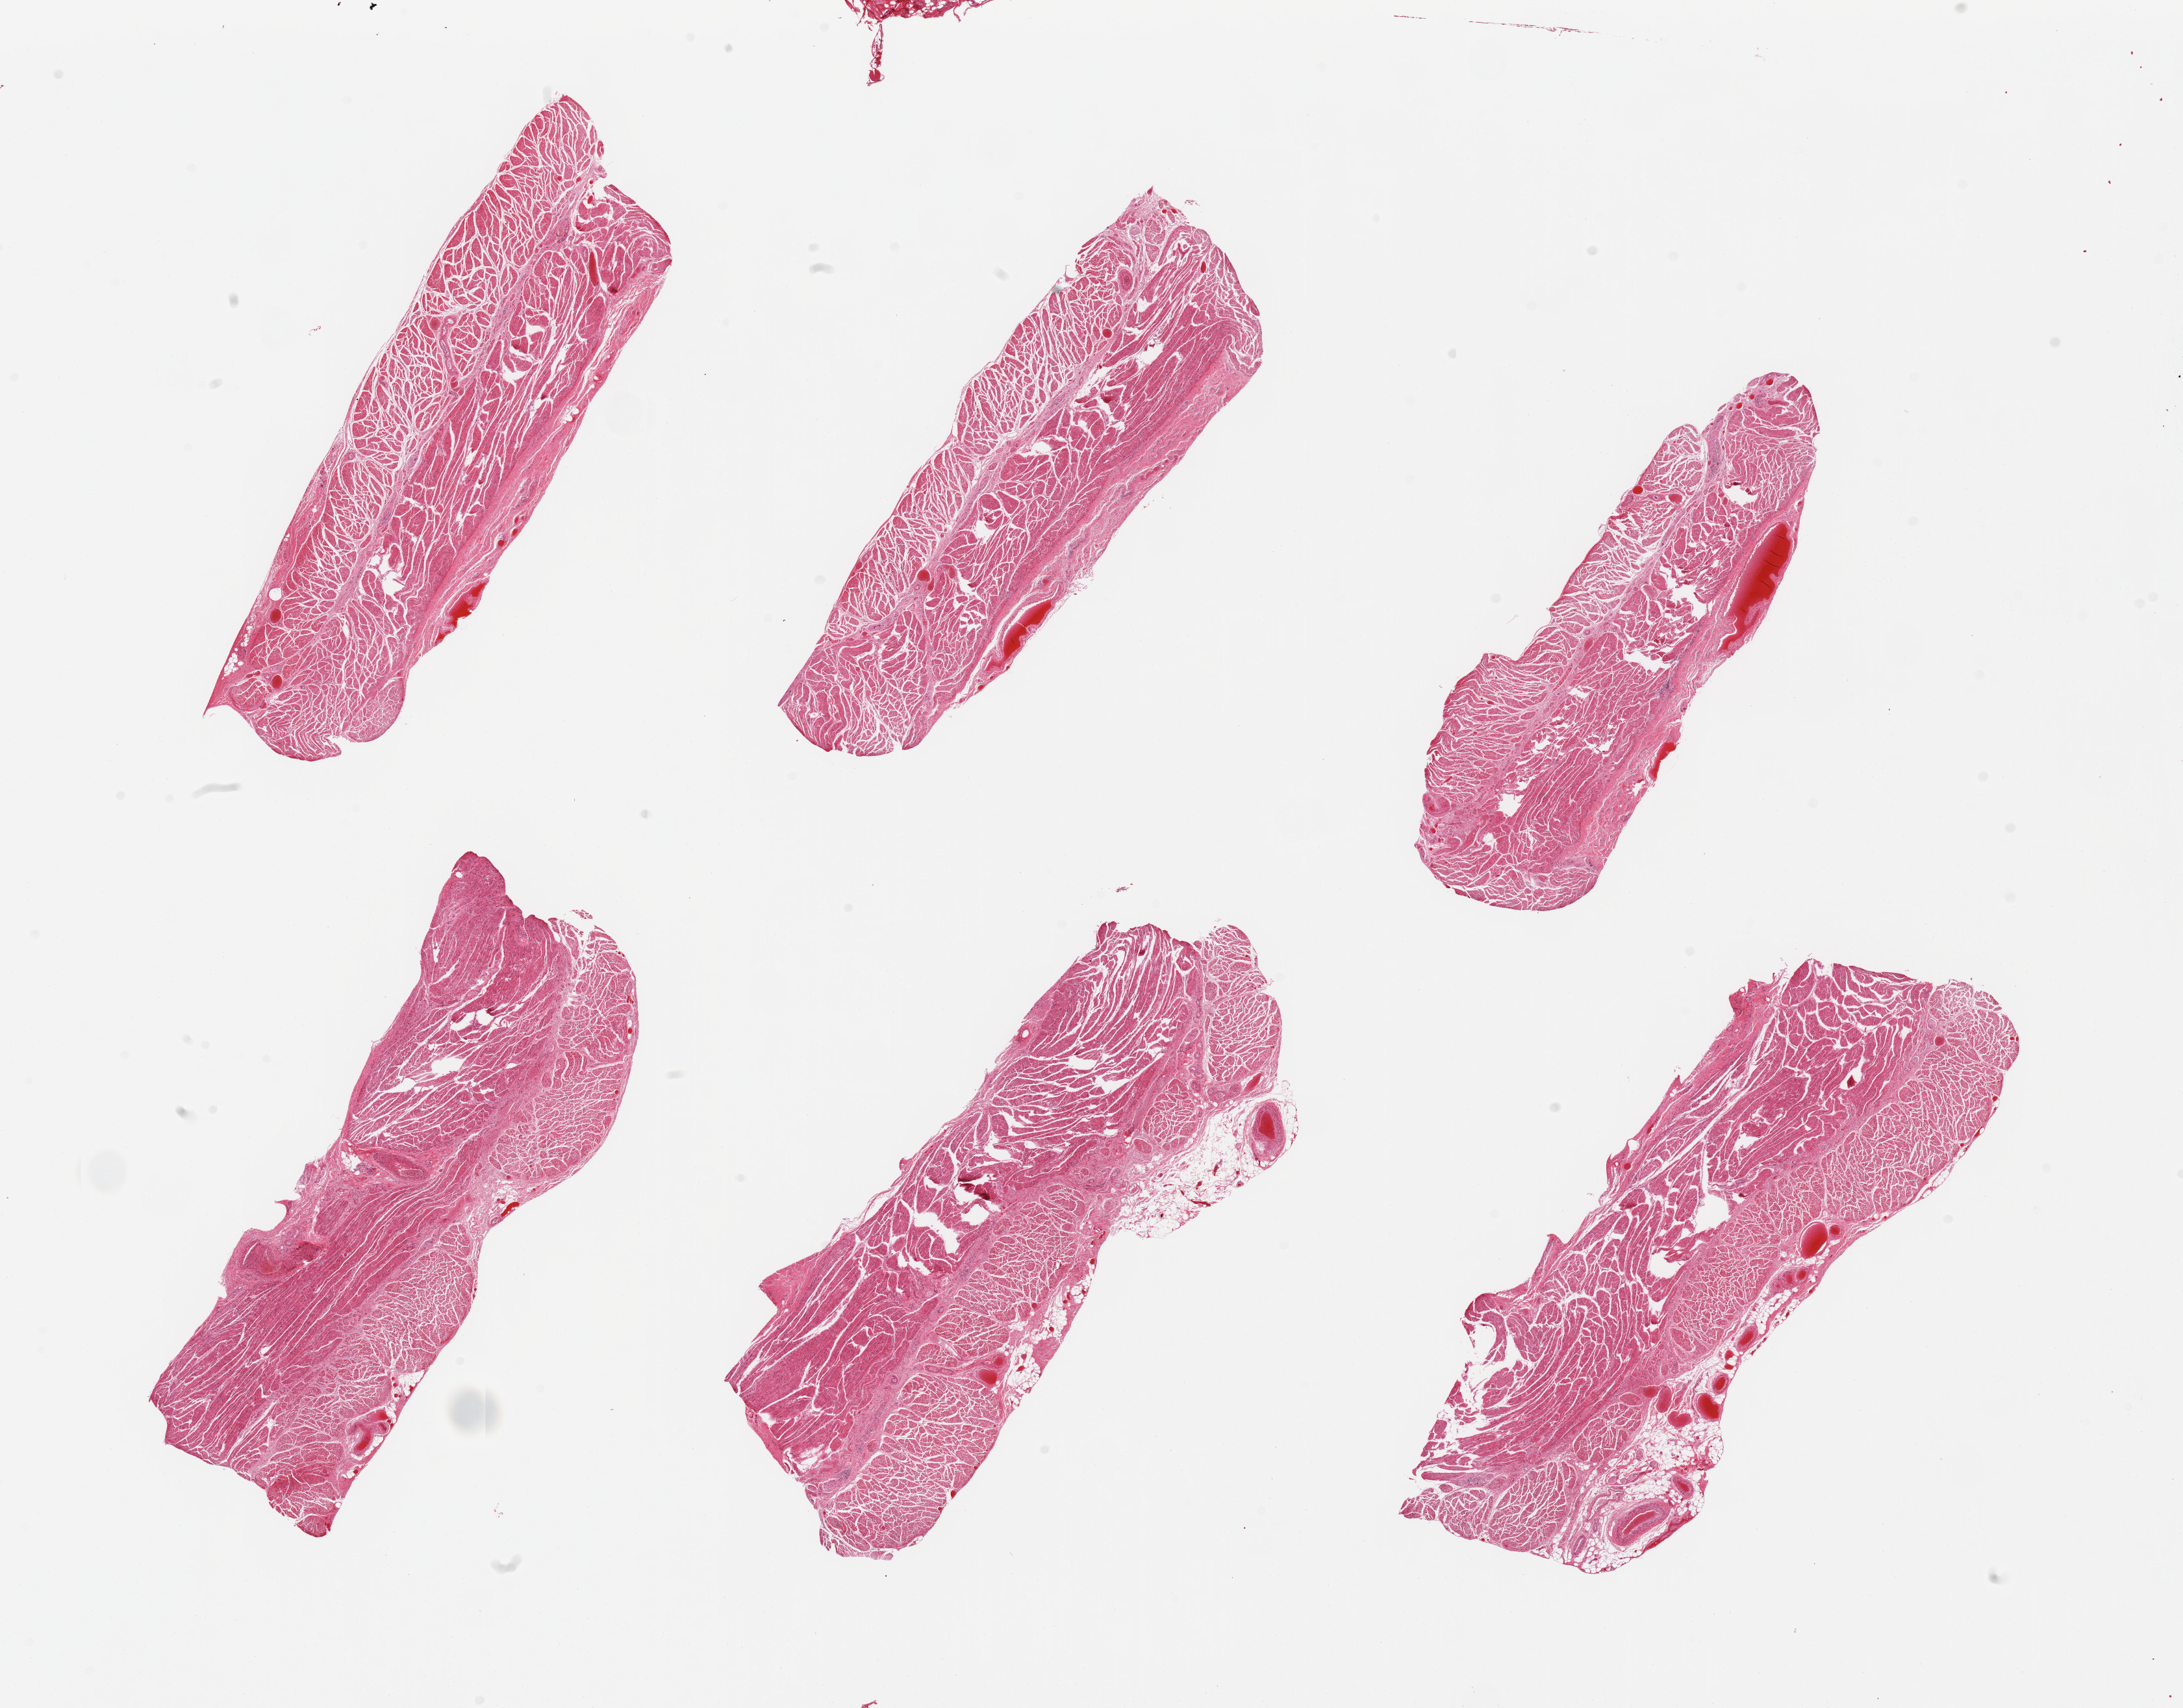
Whole-slide image, haematoxylin and eosin stain, low-resolution overview of the scanned area, about 26.6 x 20.8 mm, PAXgene-fixed, paraffin-embedded tissue, target tissue: esophageal muscle, donor tissue sample. Donor: male.
Review note (as recorded): 6 pieces; 2 pieces have 10% external fat.